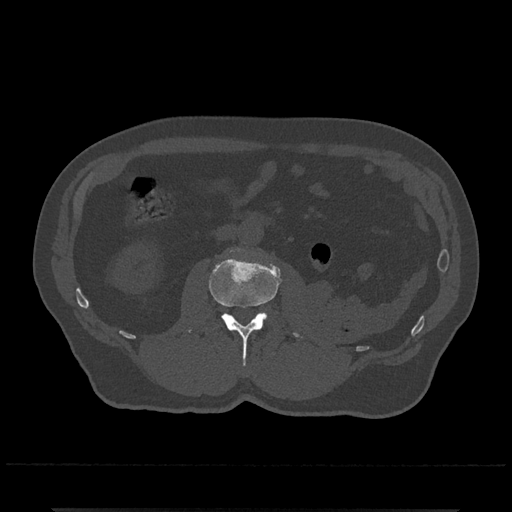
CT including the spine, one axial slice. Slice 282 of 797 in the series (ordered by position). Reconstruction kernel Br40s/3. 120 kVp. Bone window (W 1800 / L 400 HU). 0.5 mm slice thickness. 512 × 512 image matrix. Patient: male, 67 years. Case-level facts recorded for this patient, not image findings: primary cancer: prostate.
Annotated regions visible in this slice (semi-automatically segmented with operator editing):
- L2 vertebra: bounding box [x1, y1, x2, y2] px = [188, 247, 301, 366]
- L3 vertebra: [258, 312, 267, 315]